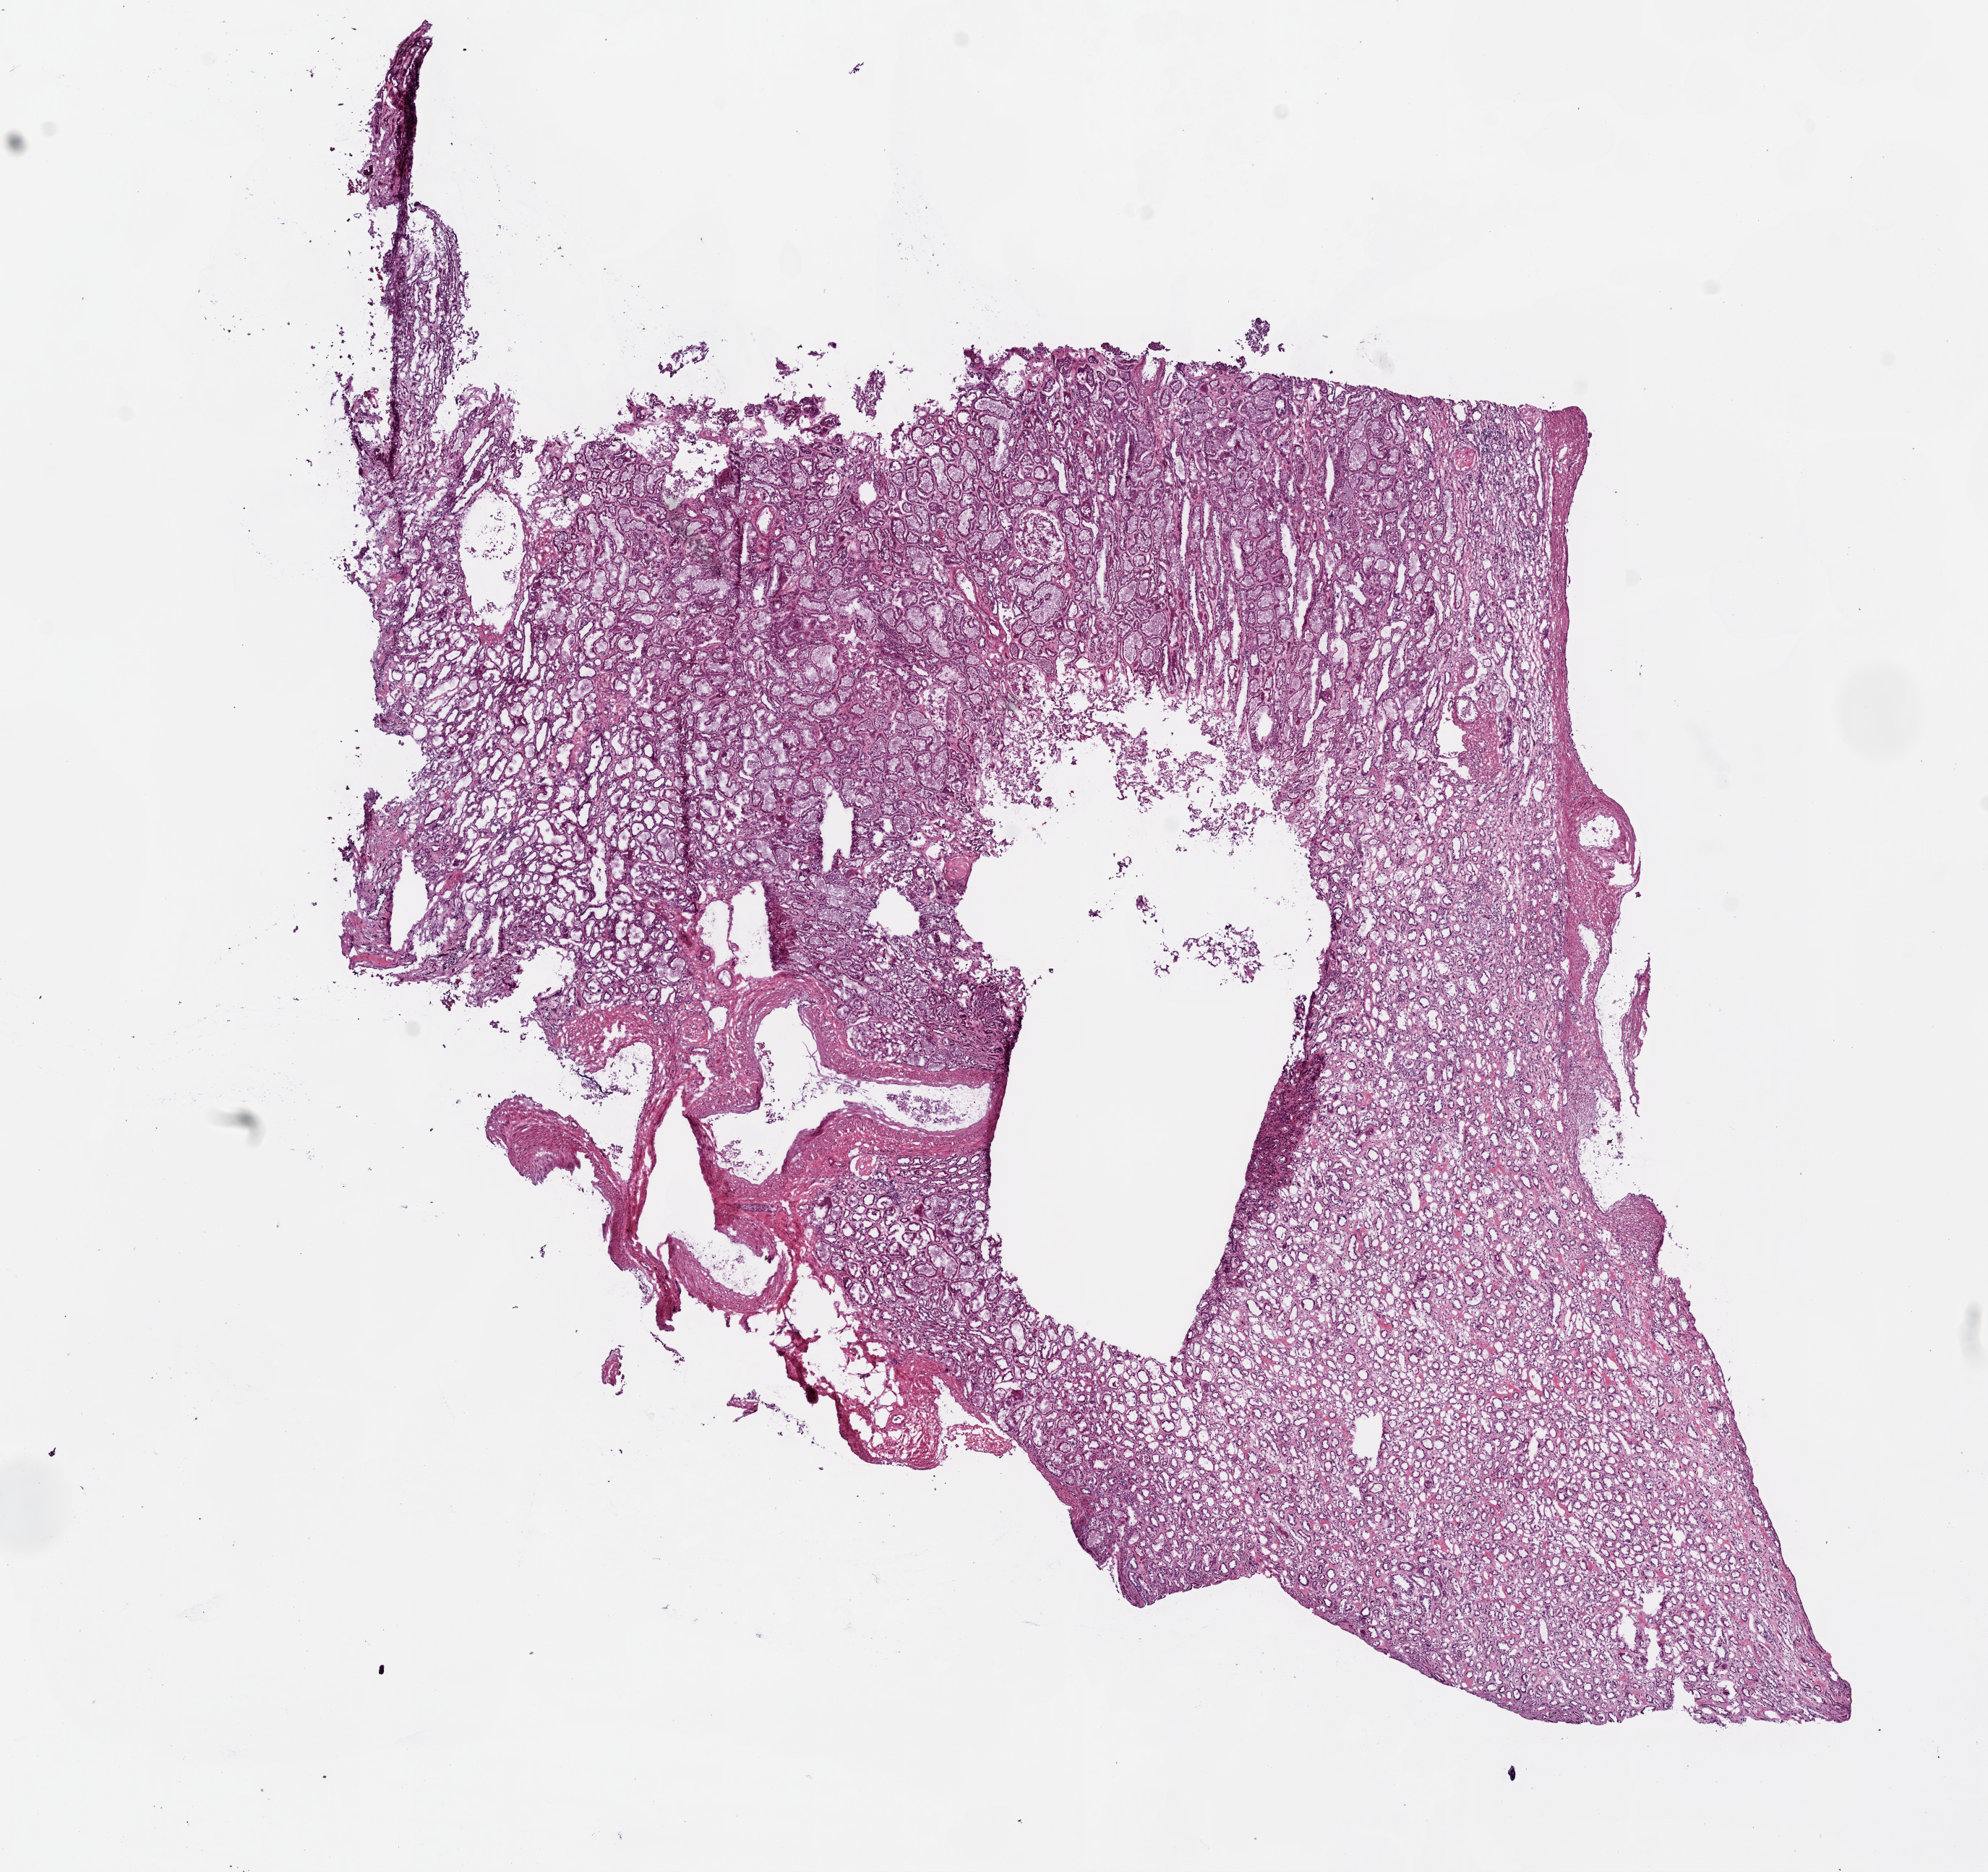
Digitized H&E tissue section (whole slide), whole scanned area (about 11.0 x 10.4 mm) shown as a low-resolution overview, frozen section from the bottom of the tissue portion, sample: solid tissue normal (non-tumour tissue), kidney. Patient: female, age at initial diagnosis 68 years.
This section: solid tissue normal sample (biorepository sample class). Patient diagnosis: Clear cell adenocarcinoma, NOS.